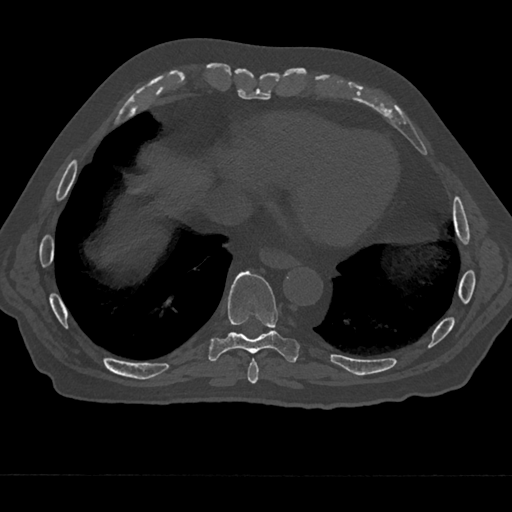
CT including the spine, one axial slice. Position 263 of 797 along the scan axis. Reconstruction kernel Br40s/3. 120 kVp. Bone window (W 1800 / L 400 HU). 512 × 512 image matrix. Patient: male, 75 years. Case-level facts recorded for this patient, not image findings: primary cancer: renal; vertebrae with lytic lesions (as recorded): T4.
Annotated regions visible in this slice (semi-automatically segmented with operator editing):
- T8 vertebra: bounding box (x1, y1, x2, y2) in pixels: (247, 358, 259, 384)
- T9 vertebra: (208, 271, 300, 363)